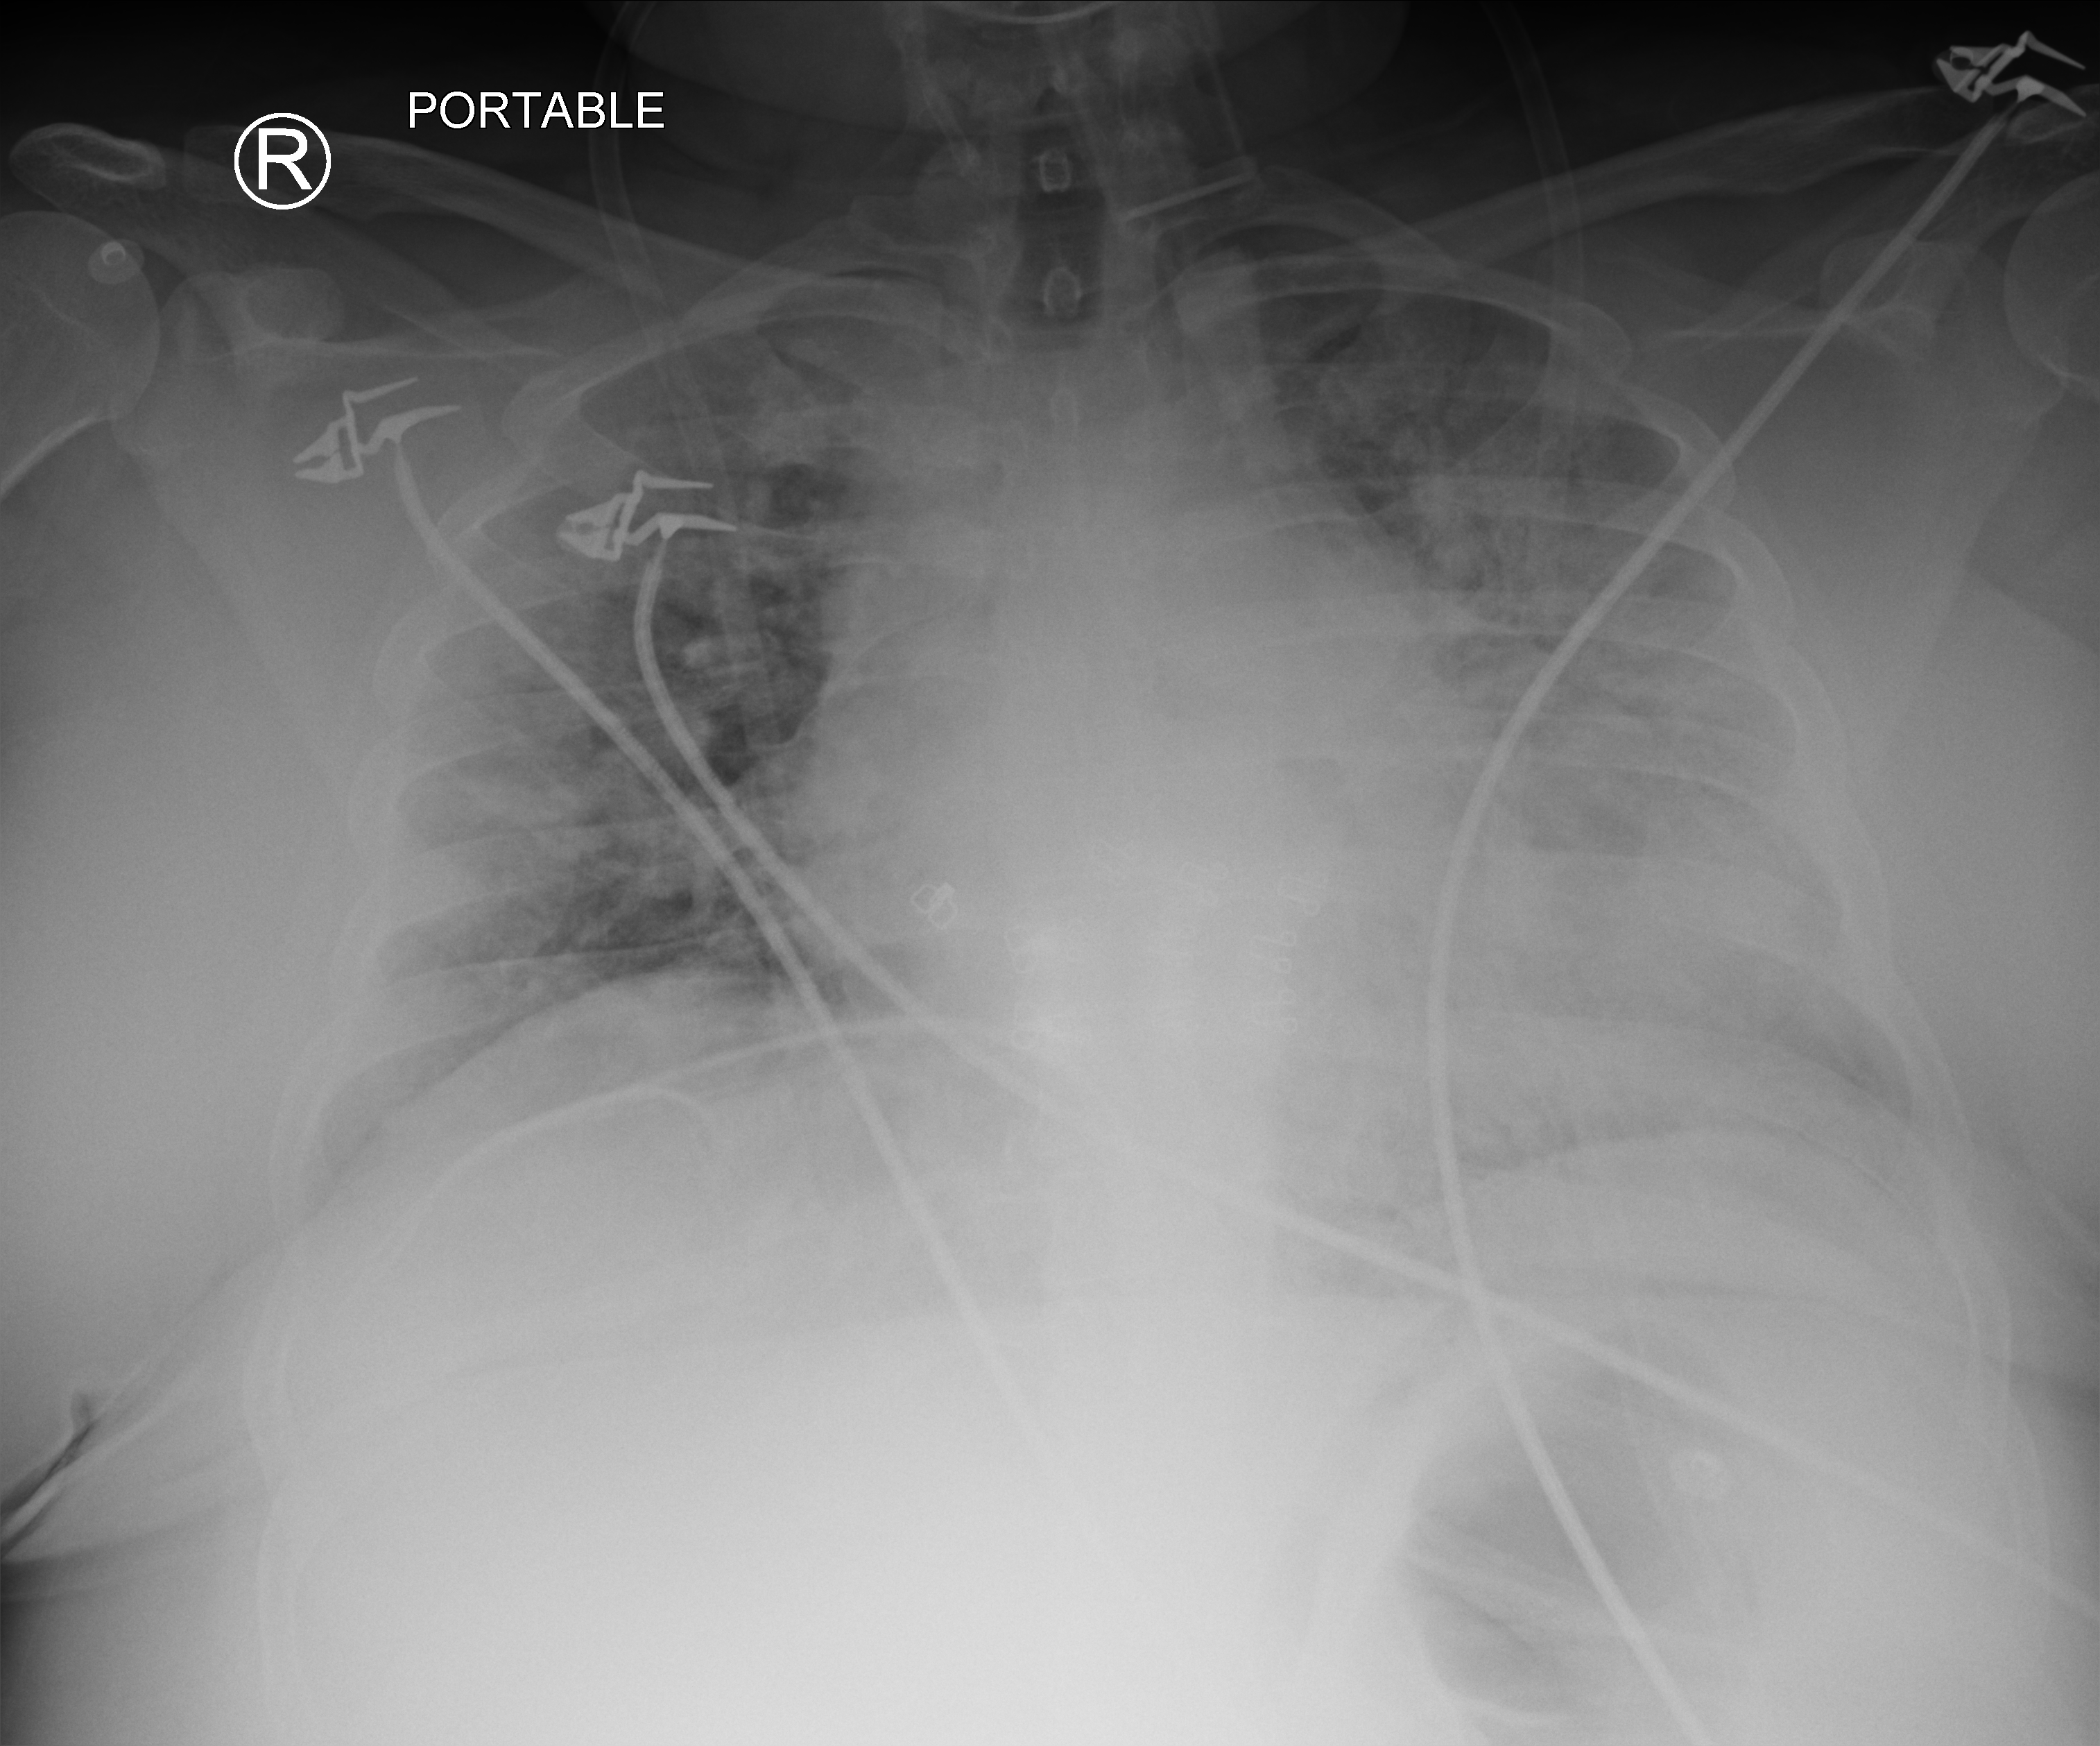
Portable chest radiograph, anteroposterior (AP) projection. Female patient hospitalised with COVID-19, age 18–59 years.
Admission-level facts for this patient (not findings on this image; timing relative to this image not recorded): hypertension (admission record): yes.